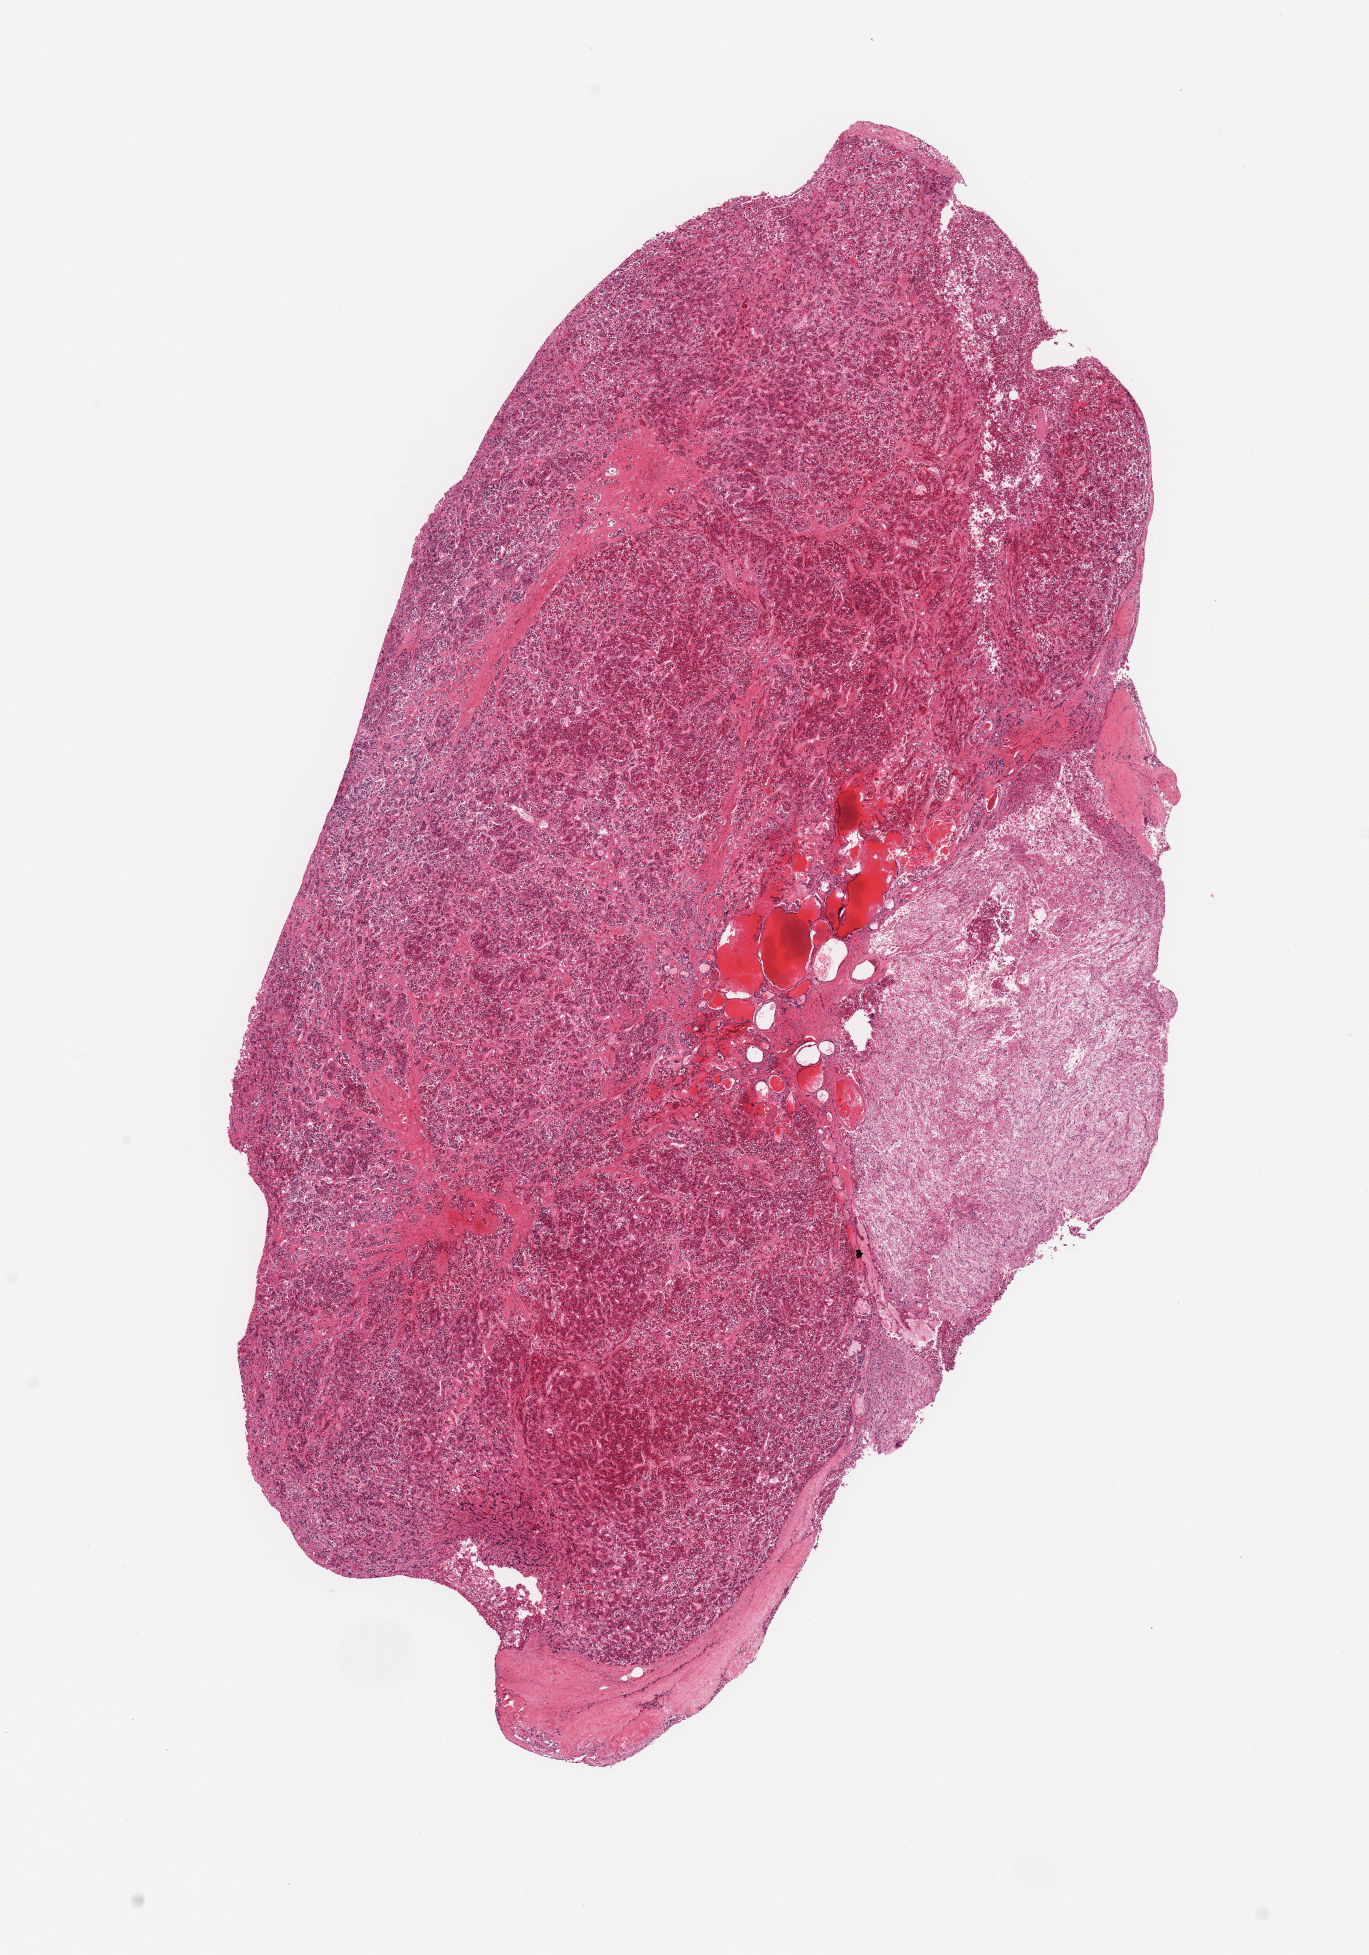
Digitized hematoxylin and eosin (H&E)-stained section, low-resolution overview of the scanned area, about 10.8 x 15.5 mm (slide scanned at 20x); PAXgene-fixed paraffin-embedded (PFPE) section; sampled site (target tissue): pituitary; donor tissue sample. Donor: male.
Review note (as recorded): 1 piece; neurohypophysis.